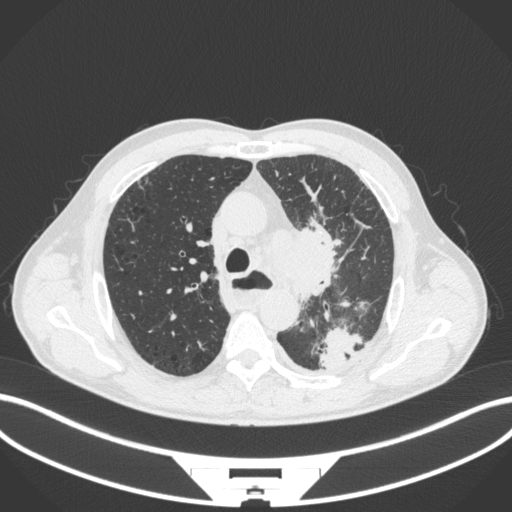
Chest CT, one axial slice. Position 270 of 411 along the scan axis. Reconstruction kernel B31f. 120 kVp. Lung window (W 1500 / L -600 HU). 1 mm slice thickness. 512 × 512 image matrix, field of view 400 × 400 mm. Male patient, age 57 years. From the clinical record (not read from this slice): clinical TNM (as recorded): T2a N1 M0.
Annotated regions visible in this slice (bounding box drawn by a radiologist):
- lung tumour (recorded histology: squamous cell carcinoma): bounding box <261,217,348,300> (left, top, right, bottom; pixels)